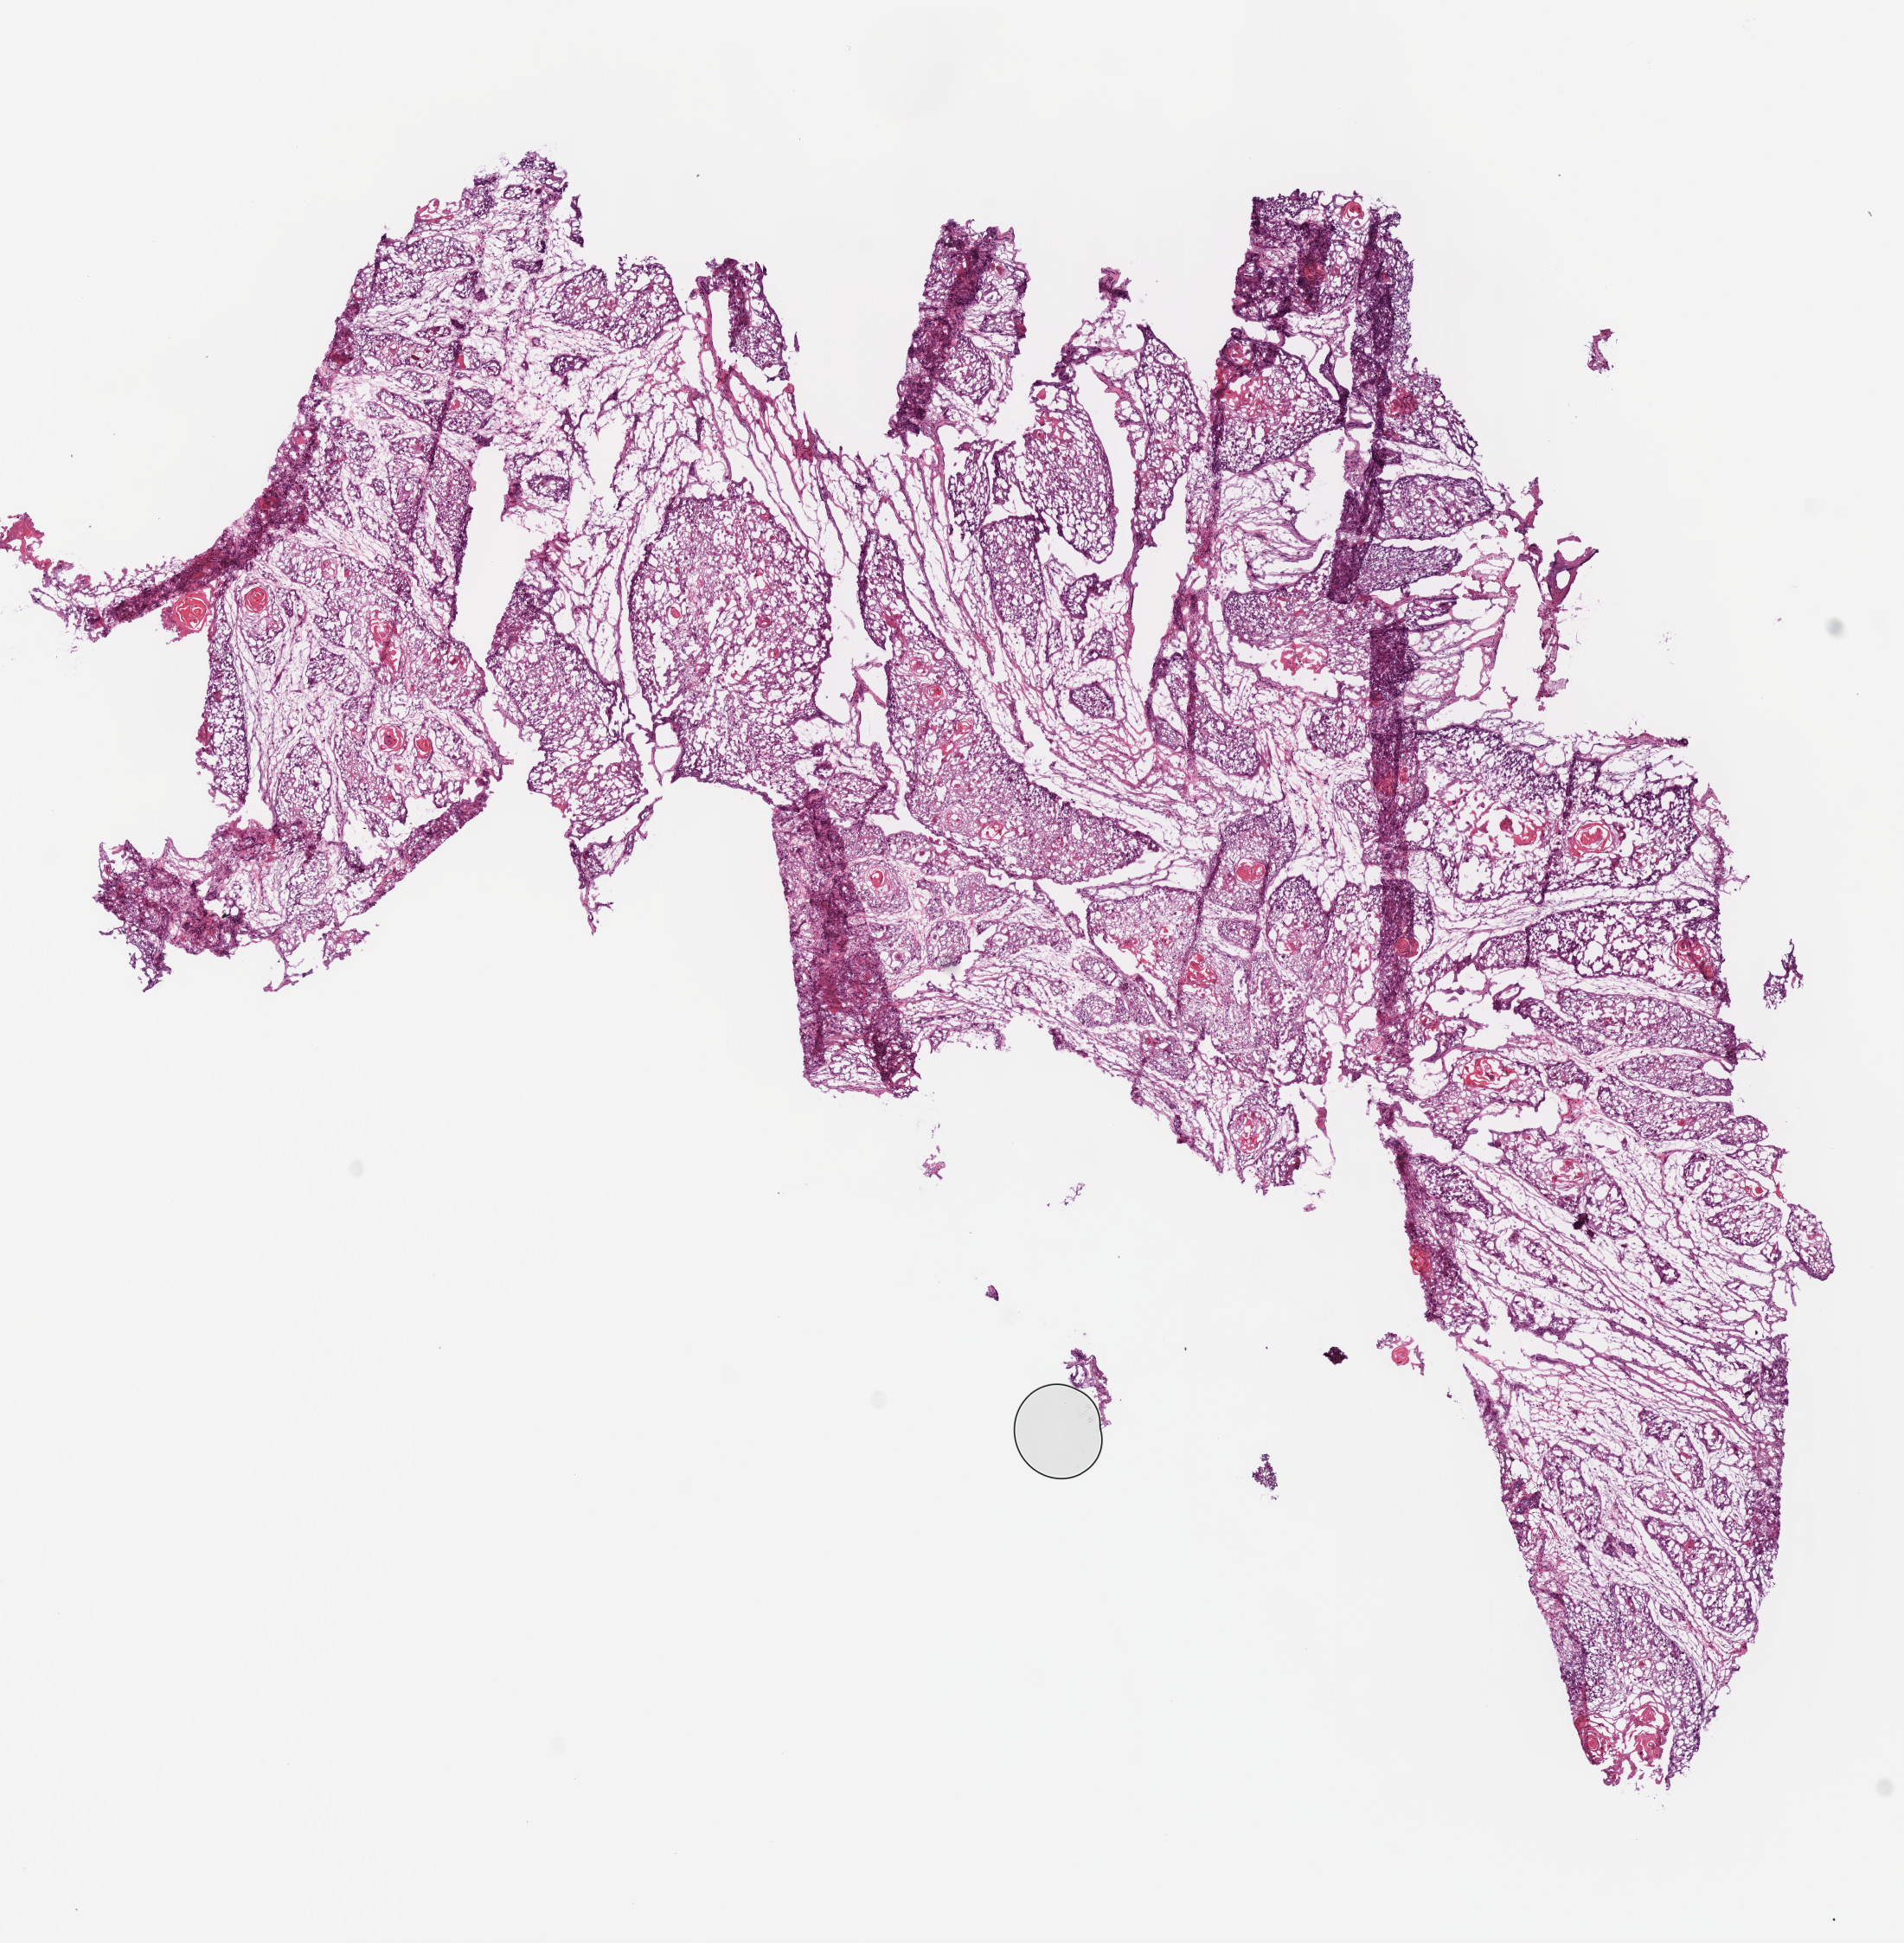
Whole-slide histology image, Hematoxylin and eosin (H&E) stained — a low-resolution overview of the entire scanned area, about 8.7 x 8.8 mm (acquisition: 40x scan). Frozen section from the bottom of the tissue portion. Sample: primary tumour, head and neck. Female patient; age at initial diagnosis 29 years. Histologic grade: GX (grade cannot be assessed). Composition of this section per pathologist review: tumour cells 100%, tumour nuclei 85%, normal cells 0%, stromal cells 0%, necrosis 0%. Infiltration values recorded for this section: lymphocyte infiltration 2%, monocyte infiltration 0%, neutrophil infiltration 0%.
- histologic diagnosis: Squamous cell carcinoma, NOS (overlapping lesion of lip, oral cavity and pharynx)
- laterality: left
- AJCC pathologic stage: IVA (7th edition)